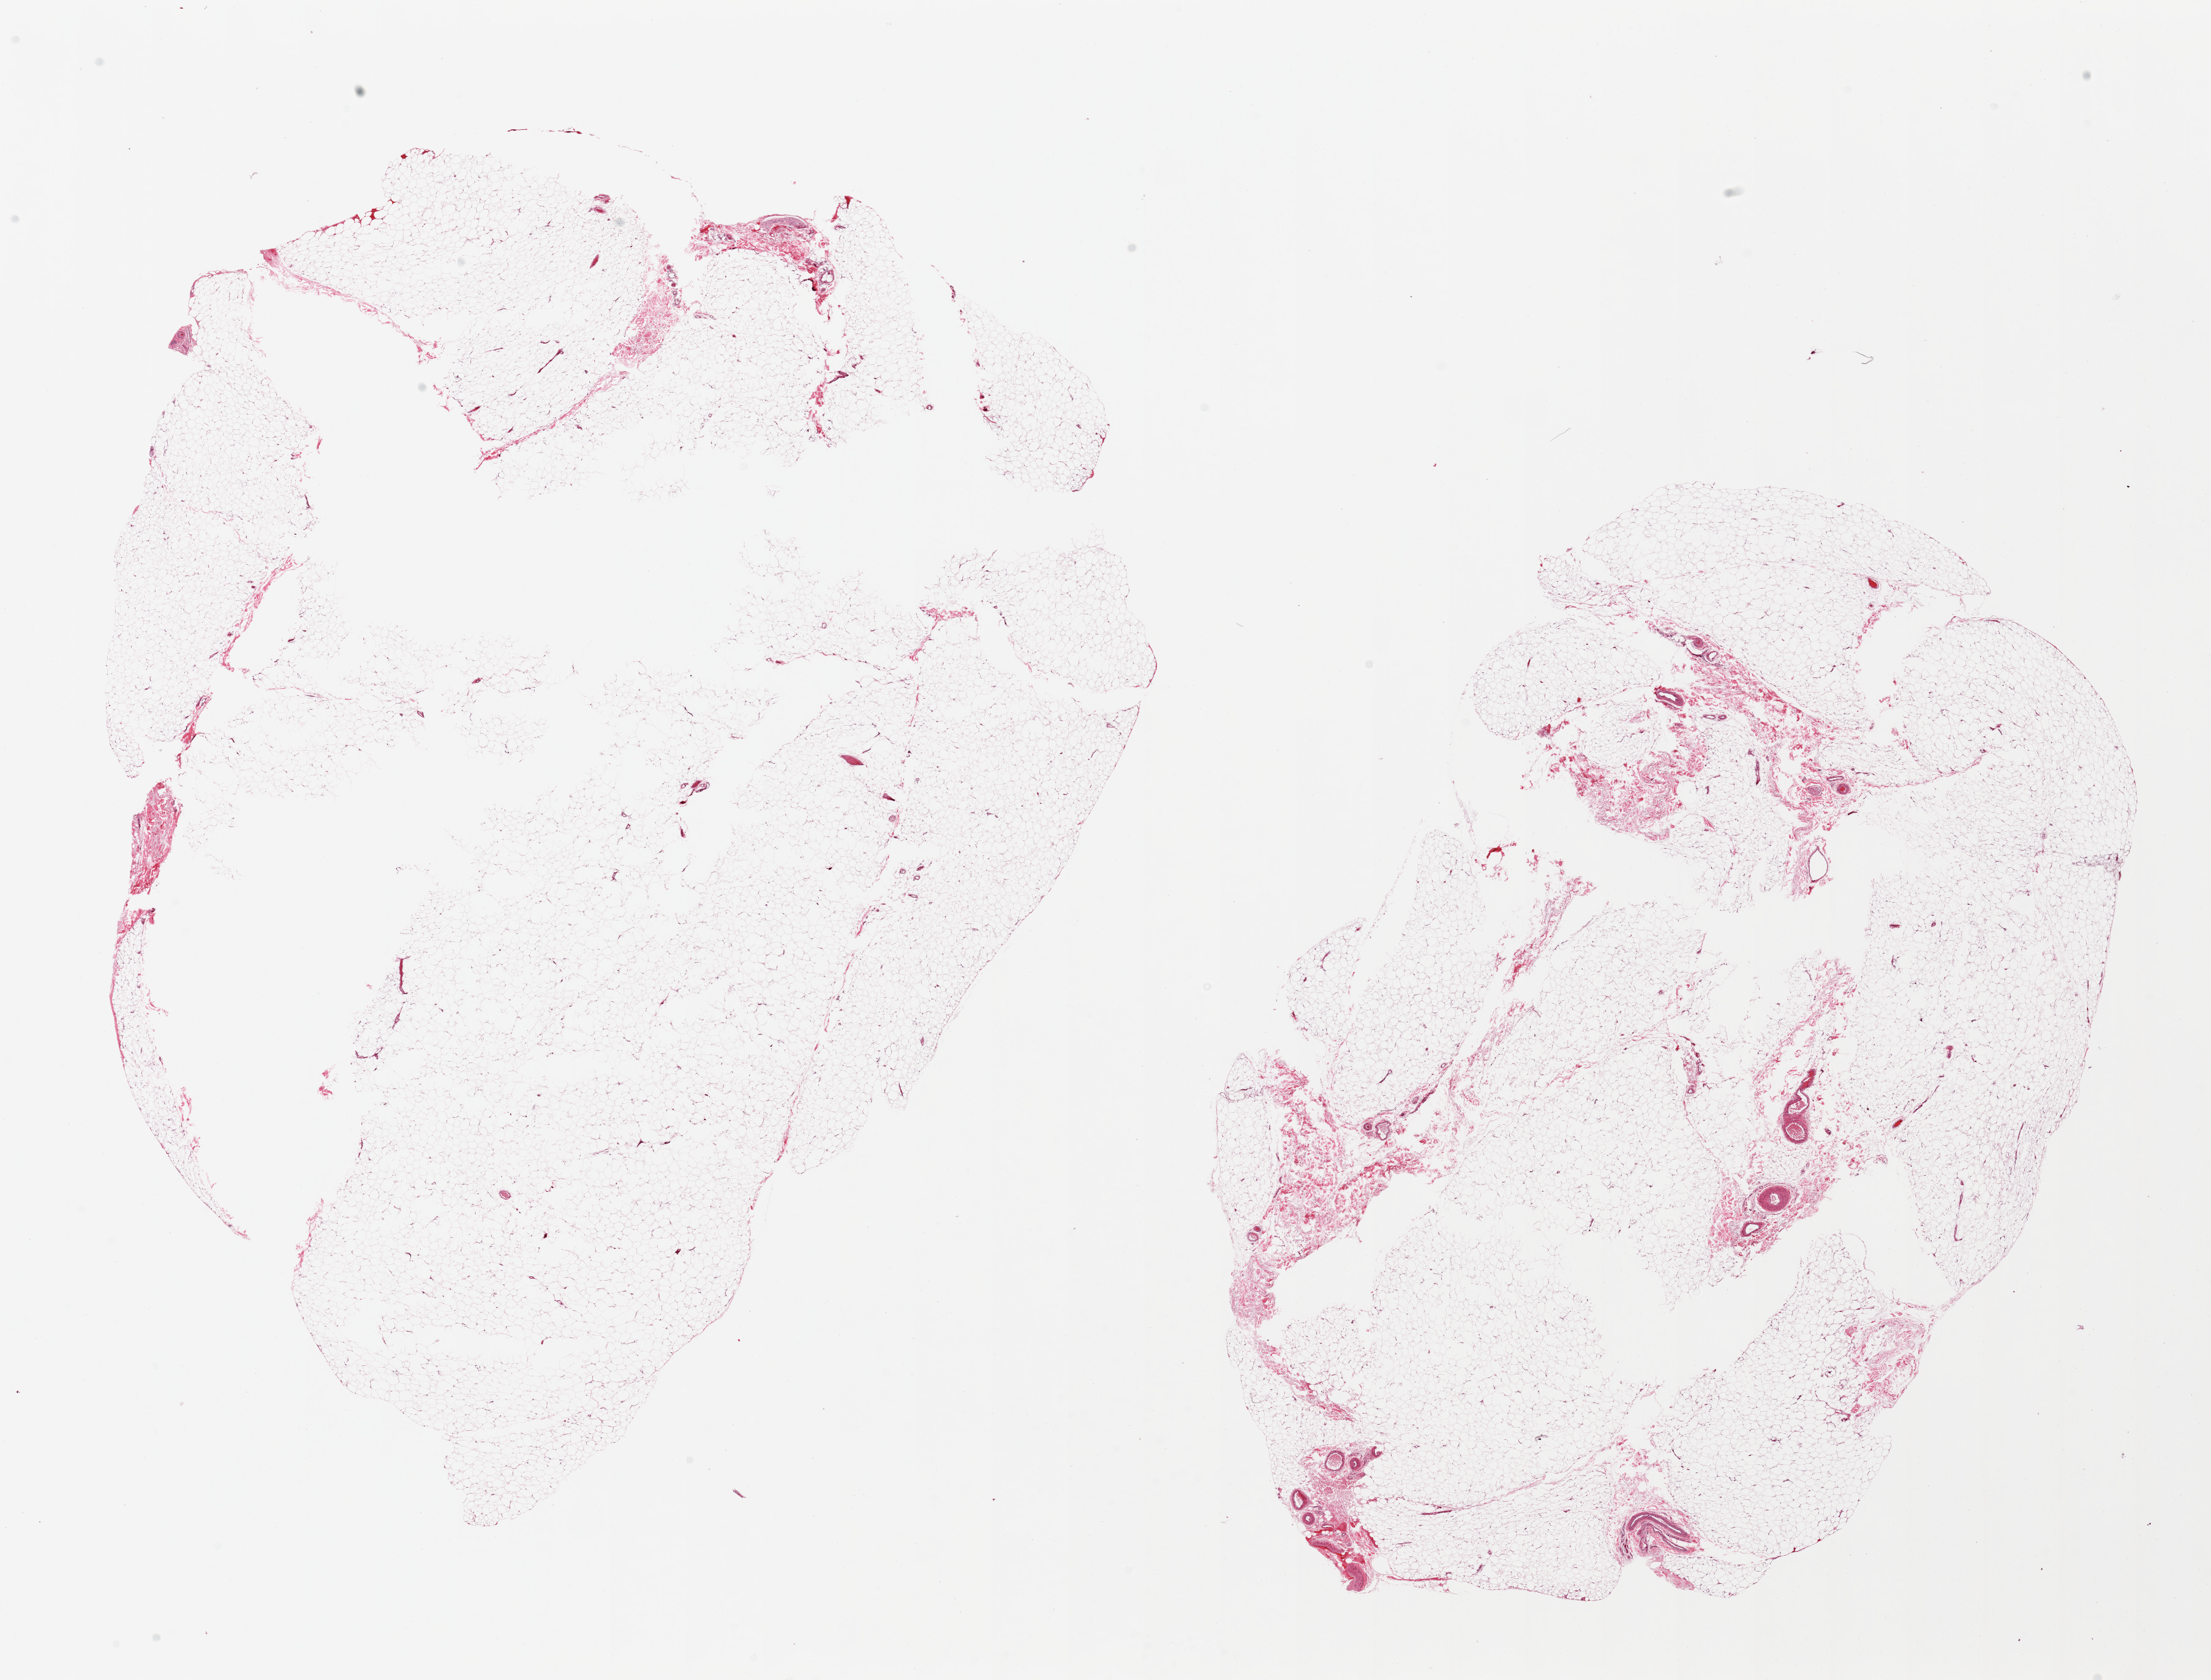
Whole-slide image, haematoxylin and eosin stain, a low-resolution overview of the entire scanned area, about 28.5 x 21.7 mm; PAXgene-fixed paraffin-embedded (PFPE) section; target tissue: adipose tissue; donor tissue sample. Donor: male.
* reviewer comment on this tissue sample: 2 pieces, overly large with central holes